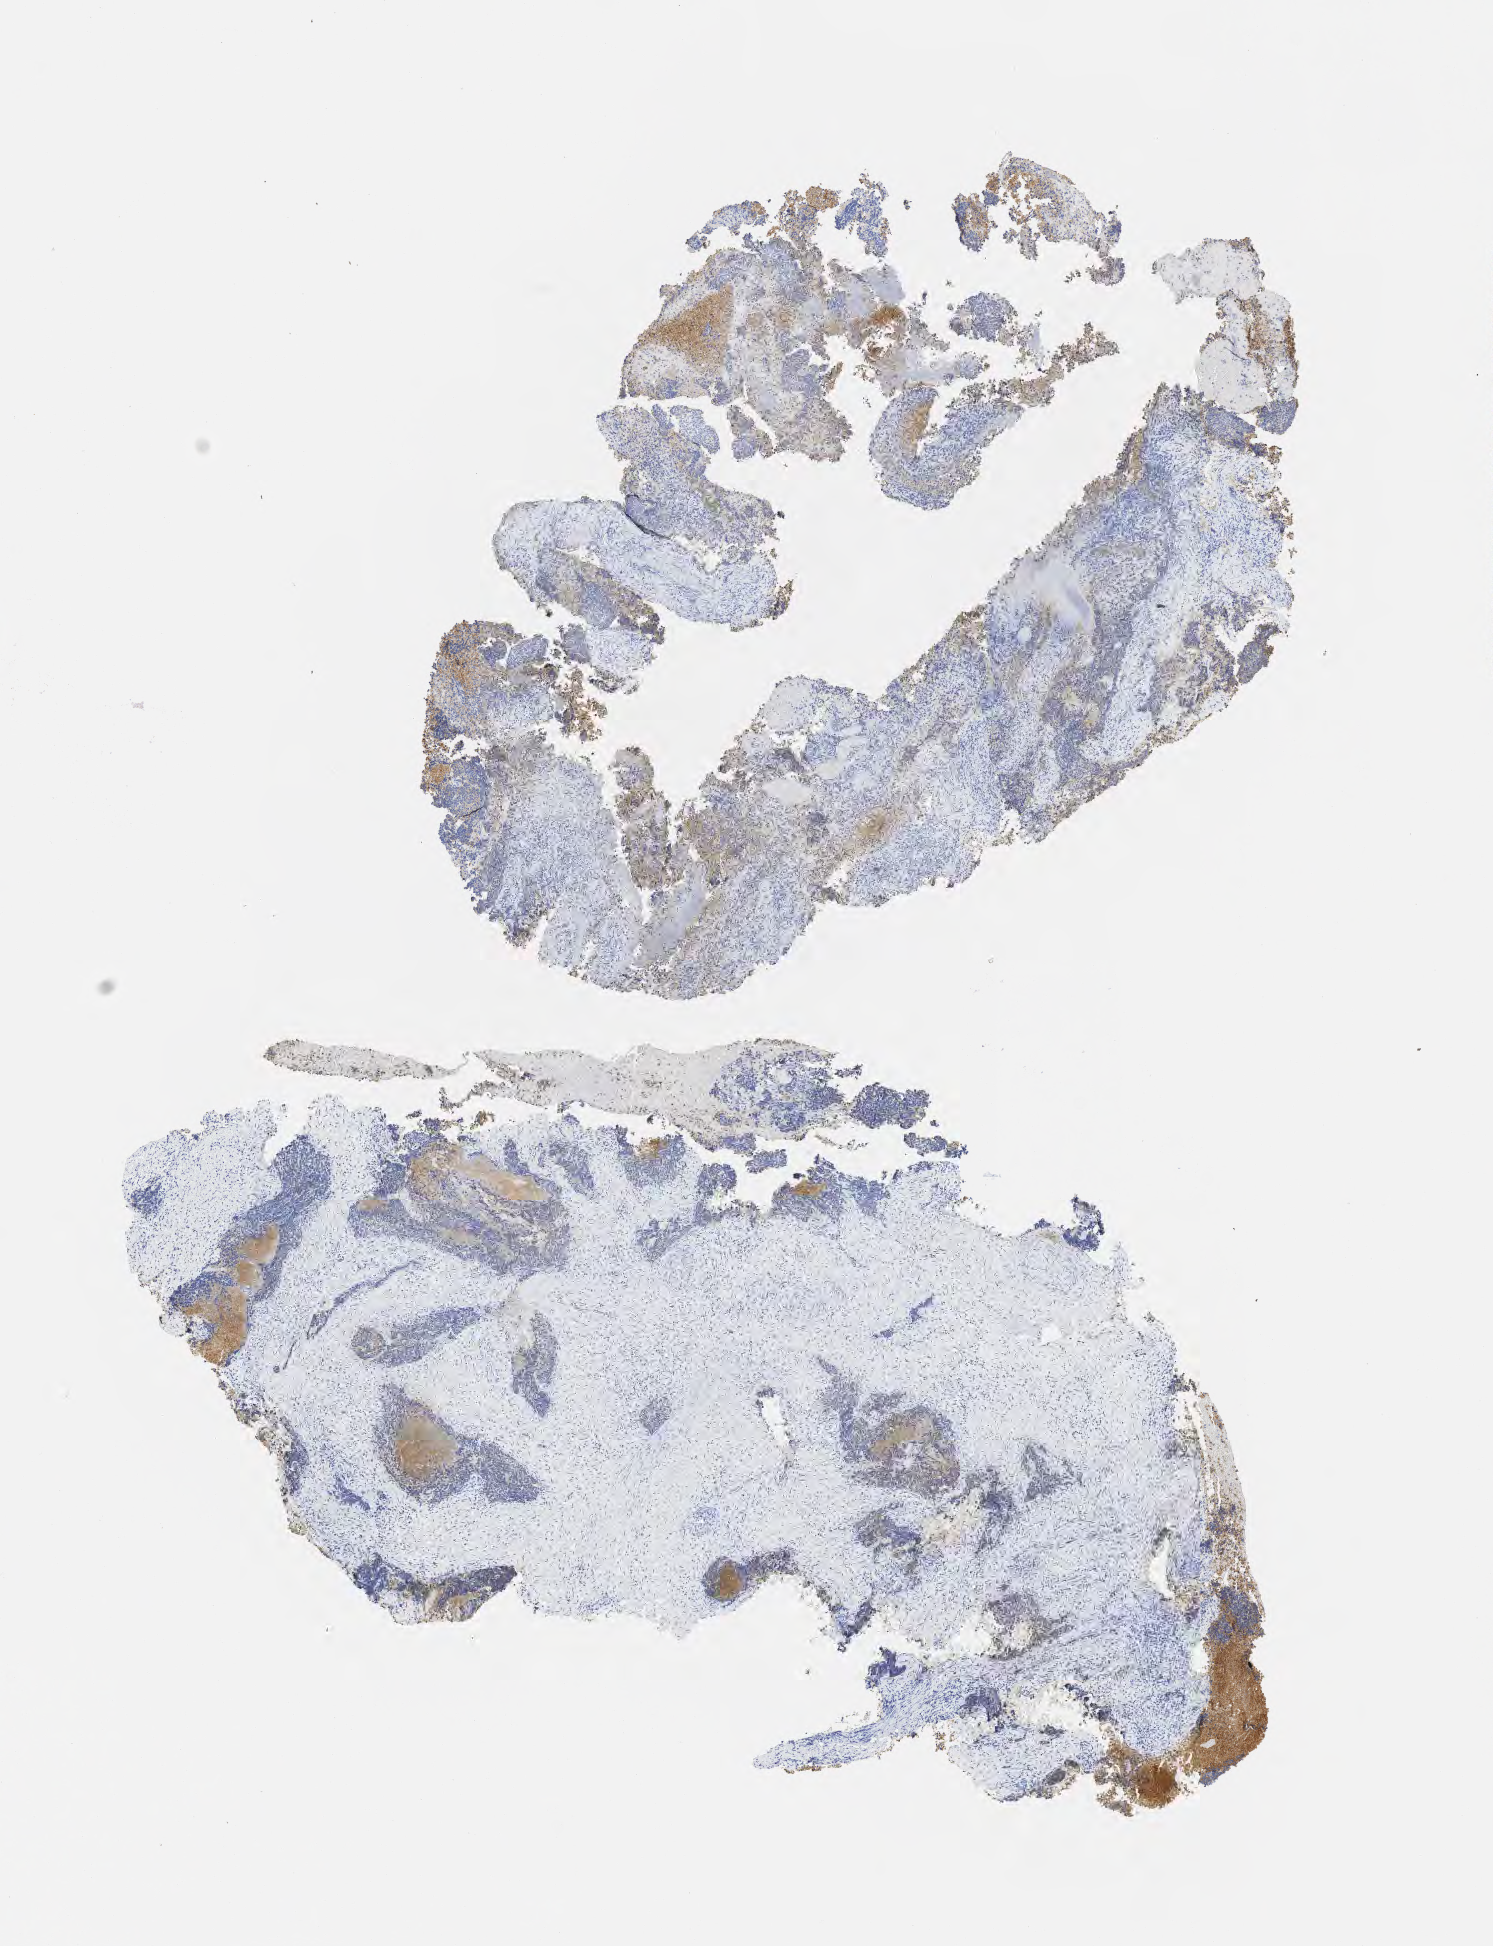
IHC for Ber-EP4, whole-slide image, whole scanned area (about 6.0 x 7.9 mm) shown as a low-resolution overview; tumor tissue; anatomic site: cervix. Patient female; aged 47.
Histologic diagnosis: Squamous cell carcinoma, large cell, nonkeratinizing, NOS.